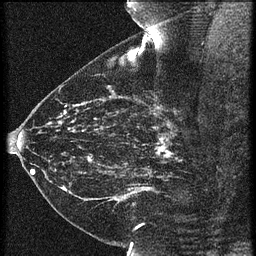
Breast MRI (dynamic contrast-enhanced), one sagittal slice. Position 38 of 60 along the scan axis. 3 images stored at this slice position (order not interpretable as contrast timing). 1.5 T. TE 4.2 ms, TR 21.3 ms. 1.5 mm slice thickness. 256 × 256 image matrix. Female patient, age 43 years. Case-level facts recorded for this patient, not image findings: setting: breast cancer imaged before/during neoadjuvant chemotherapy; receptor status: HER2-positive.
Structures marked on this image (semi-automatically segmented with operator editing):
- analysis volume of interest (the breast-tissue region the enhancement analysis was run in; not a lesion): bounding box [x1, y1, x2, y2] px = [119, 114, 189, 173]
- tumour enhancement mask (voxels above the 90 % enhancement threshold inside the analysis volume of interest): [156, 122, 181, 161]